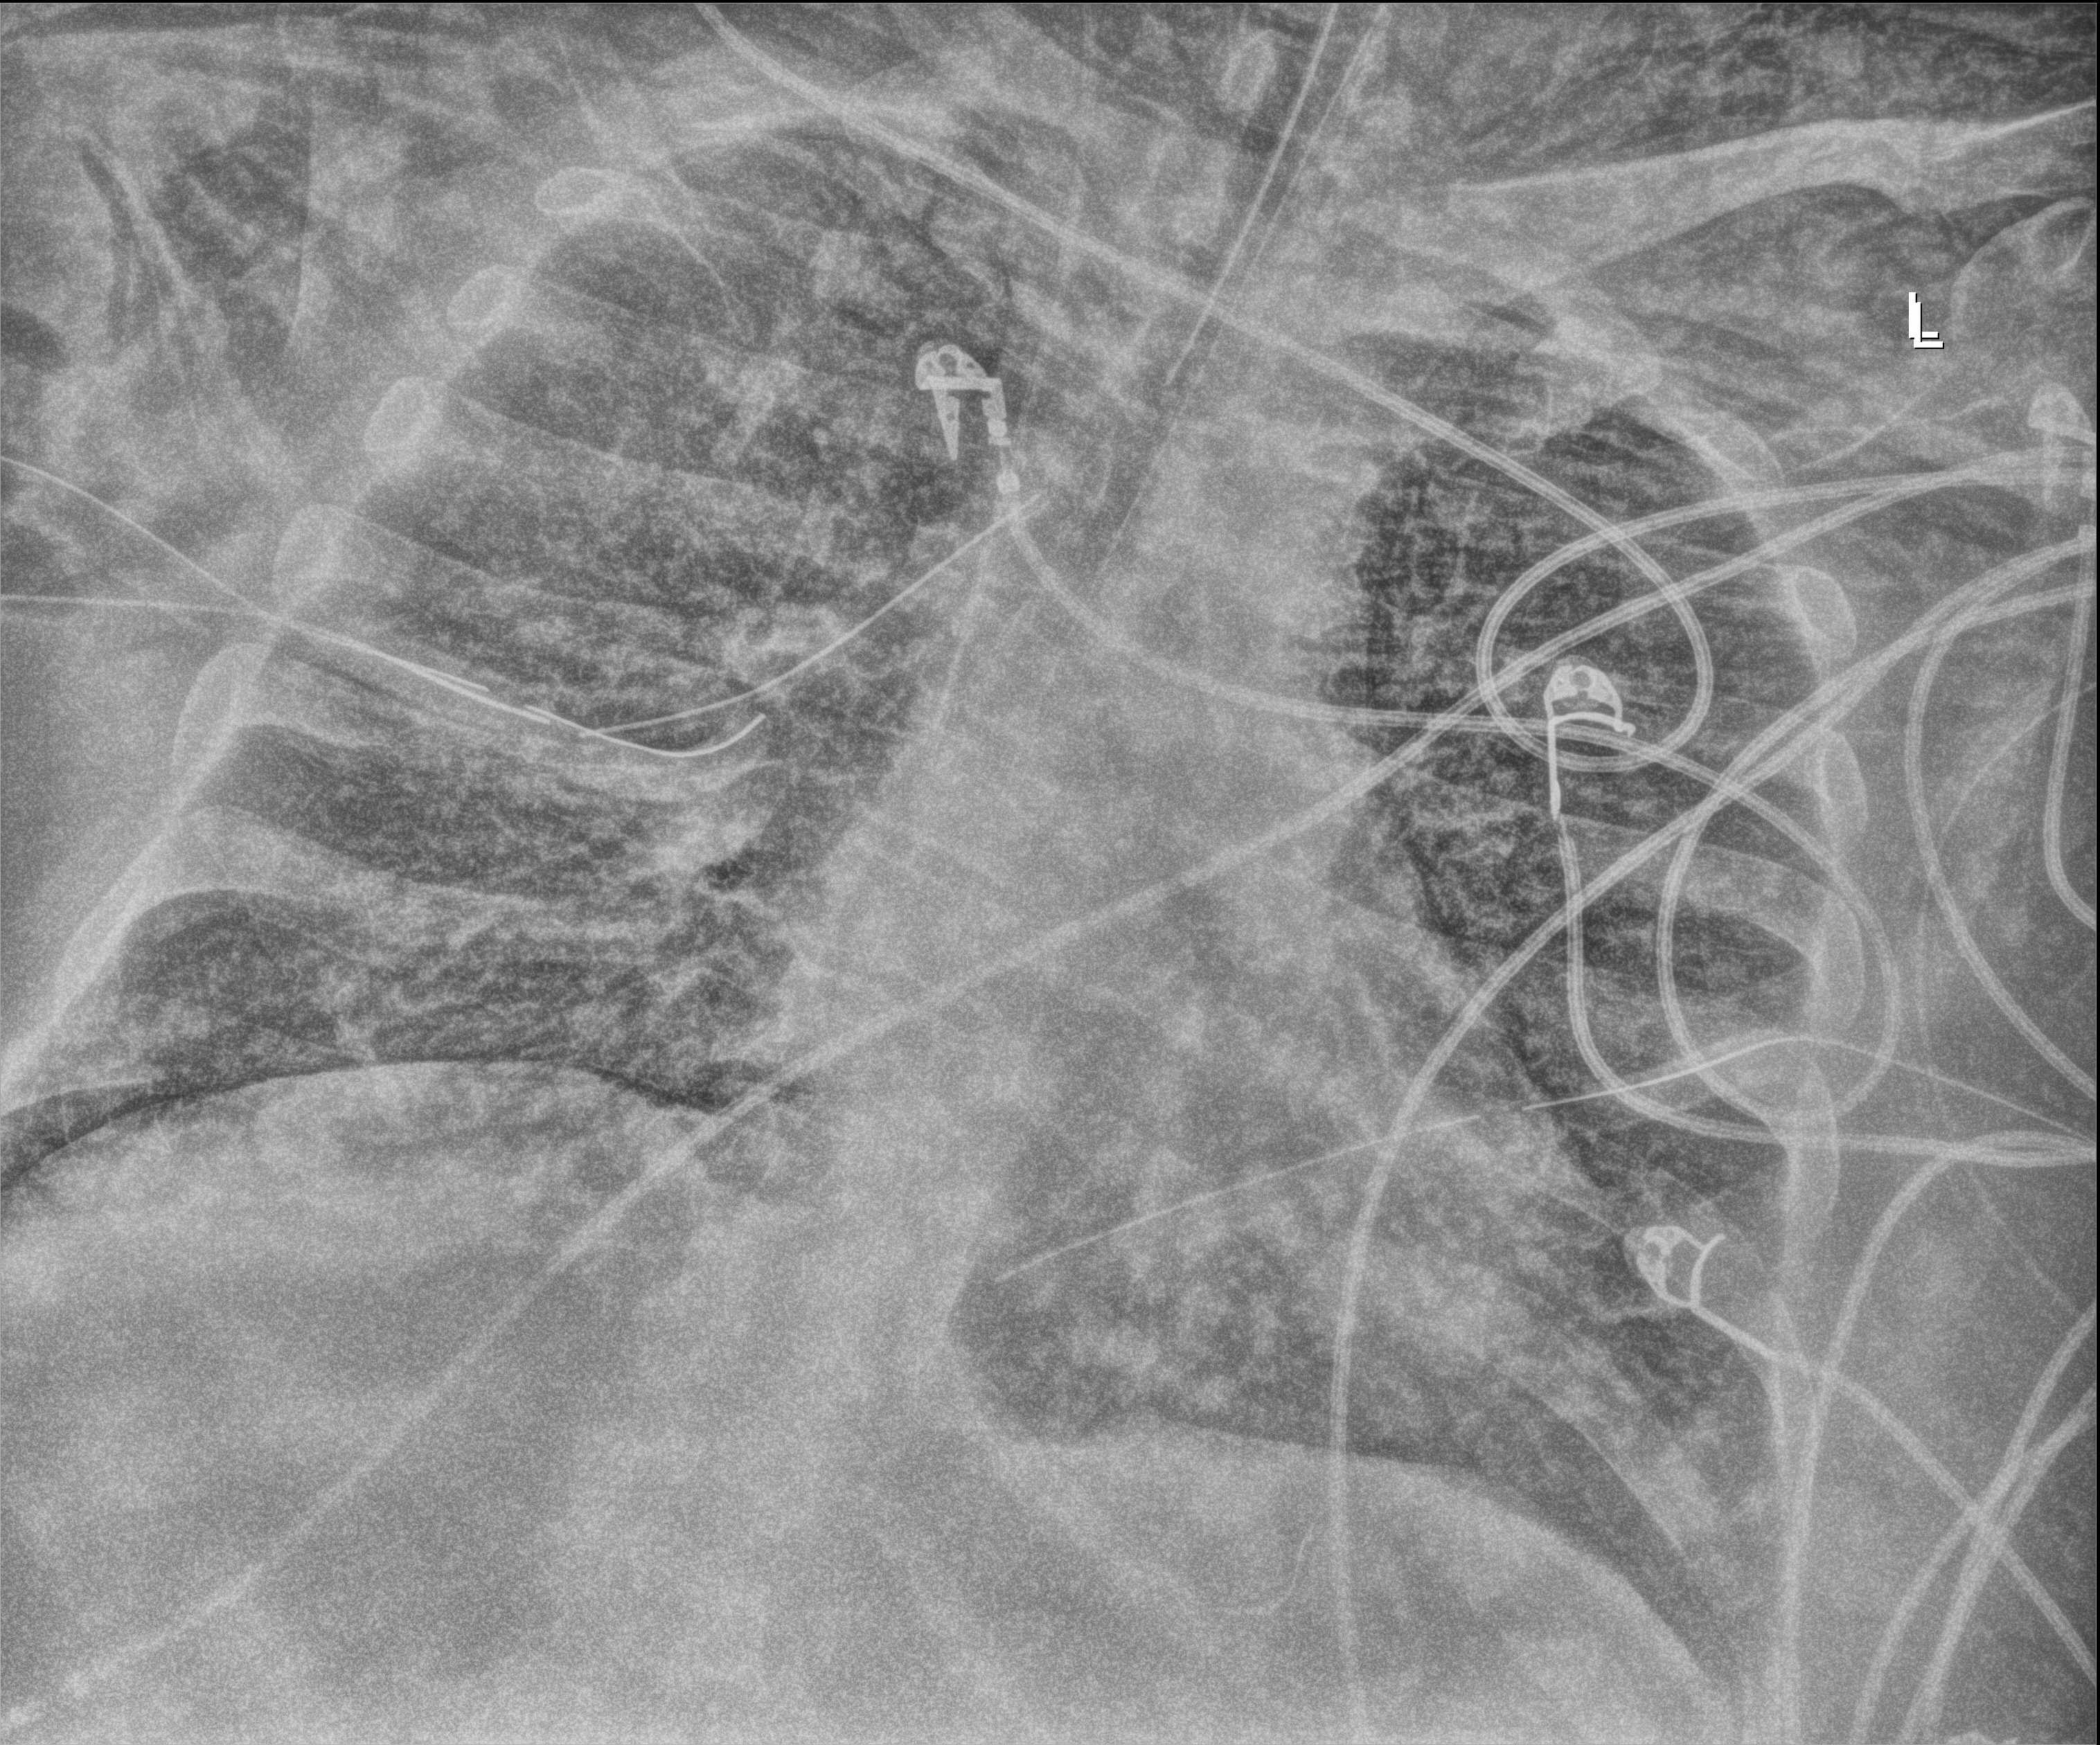
Bedside chest radiograph (digital radiography). Adult patient hospitalised with COVID-19, age 18–59 years.
Admission-level facts for this patient (not findings on this image; timing relative to this image not recorded): chronic kidney disease (admission record): no; admitted to intensive care during this hospital stay: yes.